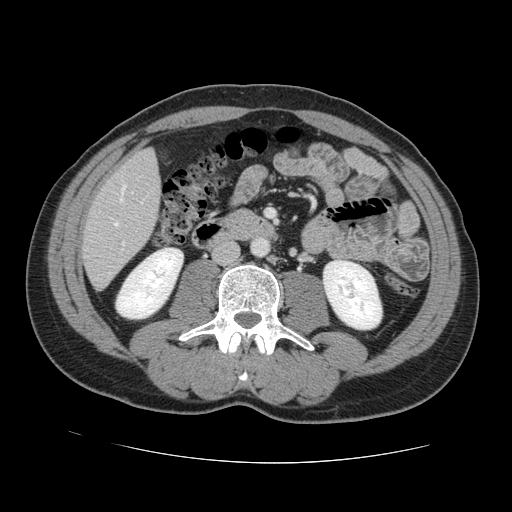
Contrast-enhanced abdominal CT, one axial slice; position 35 of 131 along the scan axis; 120 kVp; intravenous contrast given; soft-tissue window (W 400 / L 40 HU); 2.5 mm slice thickness; 512 × 512 image matrix. Male patient, age 40 years. Case-level facts recorded for this patient, not image findings: diagnosis: colorectal cancer liver metastases, imaged before liver resection; multiple liver metastases: yes; largest metastasis: 2.9 cm; chemotherapy before resection: yes.
Outlined on this slice (expert manual segmentation):
- hepatic veins: bounding box <114,186,125,226> (left, top, right, bottom; pixels)
- liver: <83,150,161,288>
- planned liver remnant (the part of the liver to remain after resection): <141,150,155,161>
- portal vein (with intrahepatic branches): <122,192,133,245>